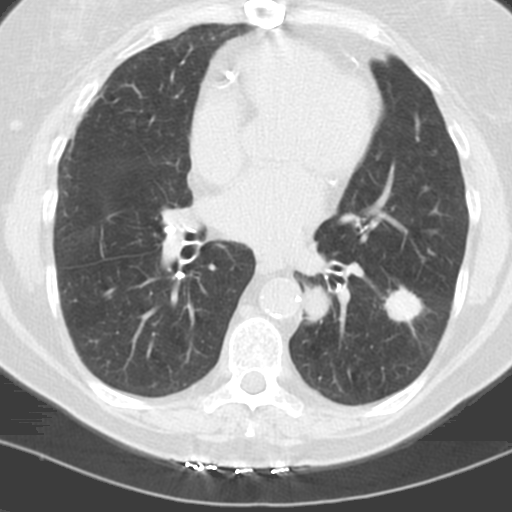
Low-dose screening chest CT, one axial slice. Position 52 of 121 along the scan axis. 120 kVp. Lung window (W 1500 / L -600 HU). 3.2 mm slice thickness. 512 × 512 image matrix, field of view 278 × 278 mm.
Structures marked on this image (expert manual segmentation):
- lesion 1 (tumor, lower lobe of left lung): bounding box (x1, y1, x2, y2) in pixels: (385, 289, 423, 322)
- lesion 2 (tumor, lower lobe of left lung): (304, 286, 331, 322)